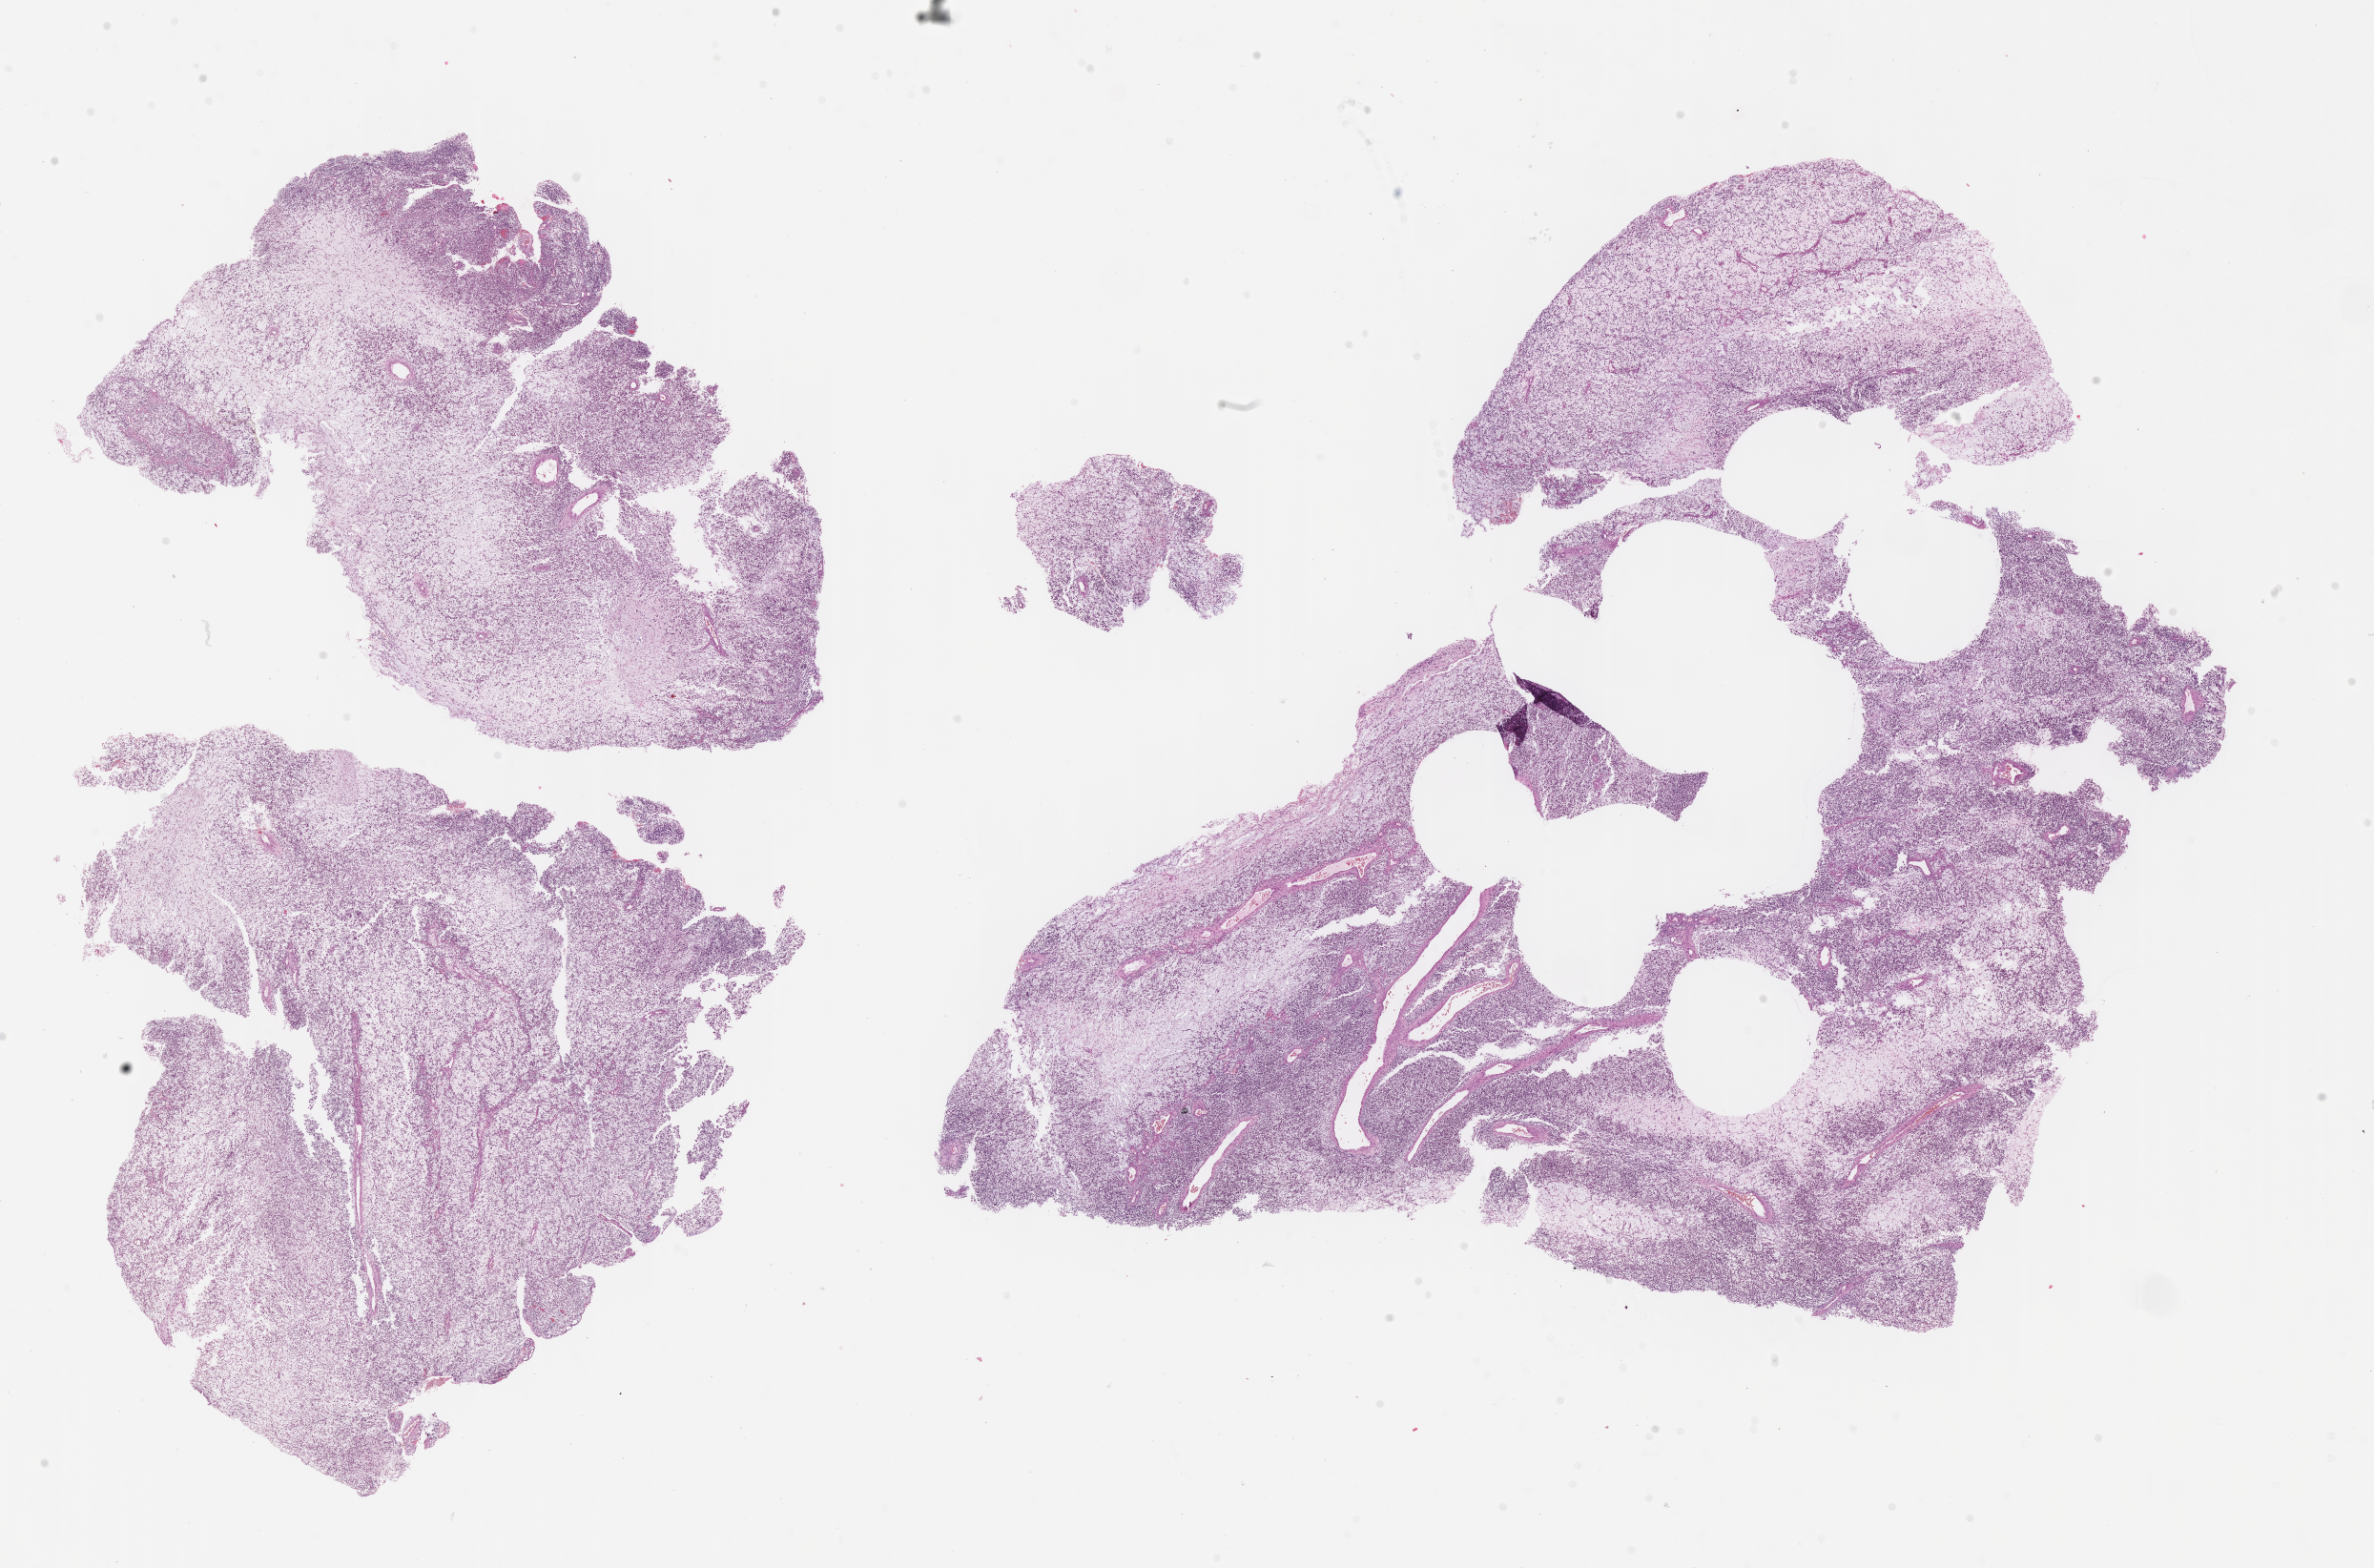
Digitized haematoxylin and eosin-stained section of tumor tissue — whole scanned area (about 20.1 x 13.3 mm) shown as a low-resolution overview. Formalin-fixed paraffin-embedded section. Site: retroperitoneum. Male patient, age at diagnosis 1.9 years.
Diagnosis: rhabdomyosarcoma; histological classification: embryonal rhabdomyosarcoma. Stage (as recorded): 3. Primary site (case record): bladder/Prostate.